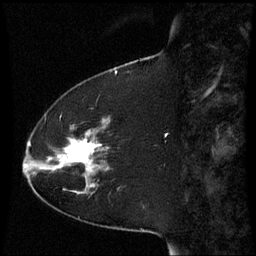
Breast MRI (dynamic contrast-enhanced), one sagittal slice; slice 15 of 60 in the series (ordered by position); dynamic contrast-enhanced series, image 2 of 3 at this slice position (ordered by acquisition); 1.5 T; TE 4.2 ms, TR 8.9 ms; 256 × 256 image matrix, field of view 210 × 210 mm. Patient: female, 51 years. From the clinical record (not read from this slice): setting: breast cancer imaged before/during neoadjuvant chemotherapy; receptor status: HR-positive, HER2-negative.
Annotated regions visible in this slice (semi-automatically segmented with operator editing):
- analysis volume of interest (the breast-tissue region the enhancement analysis was run in; not a lesion): bounding box (x1, y1, x2, y2) in pixels: (50, 119, 111, 187)
- tumour enhancement mask (voxels above the 70 % enhancement threshold inside the analysis volume of interest): (58, 141, 101, 187)